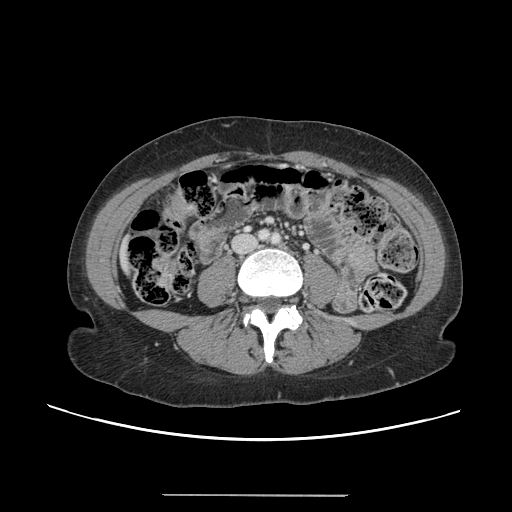
Contrast-enhanced abdominal CT, one axial slice. Position 12 of 144 along the scan axis. Intravenous contrast given. Soft-tissue window (W 400 / L 40 HU). 512 × 512 image matrix. Female patient, age 53 years. Case-level facts recorded for this patient, not image findings: diagnosis: colorectal cancer liver metastases, imaged before liver resection; multiple liver metastases: yes.
Outlined on this slice (manually delineated by an expert):
- liver: box from (x=122, y=243) to (x=128, y=270) px
- planned liver remnant (the part of the liver to remain after resection): (x=123, y=257)–(x=129, y=269)